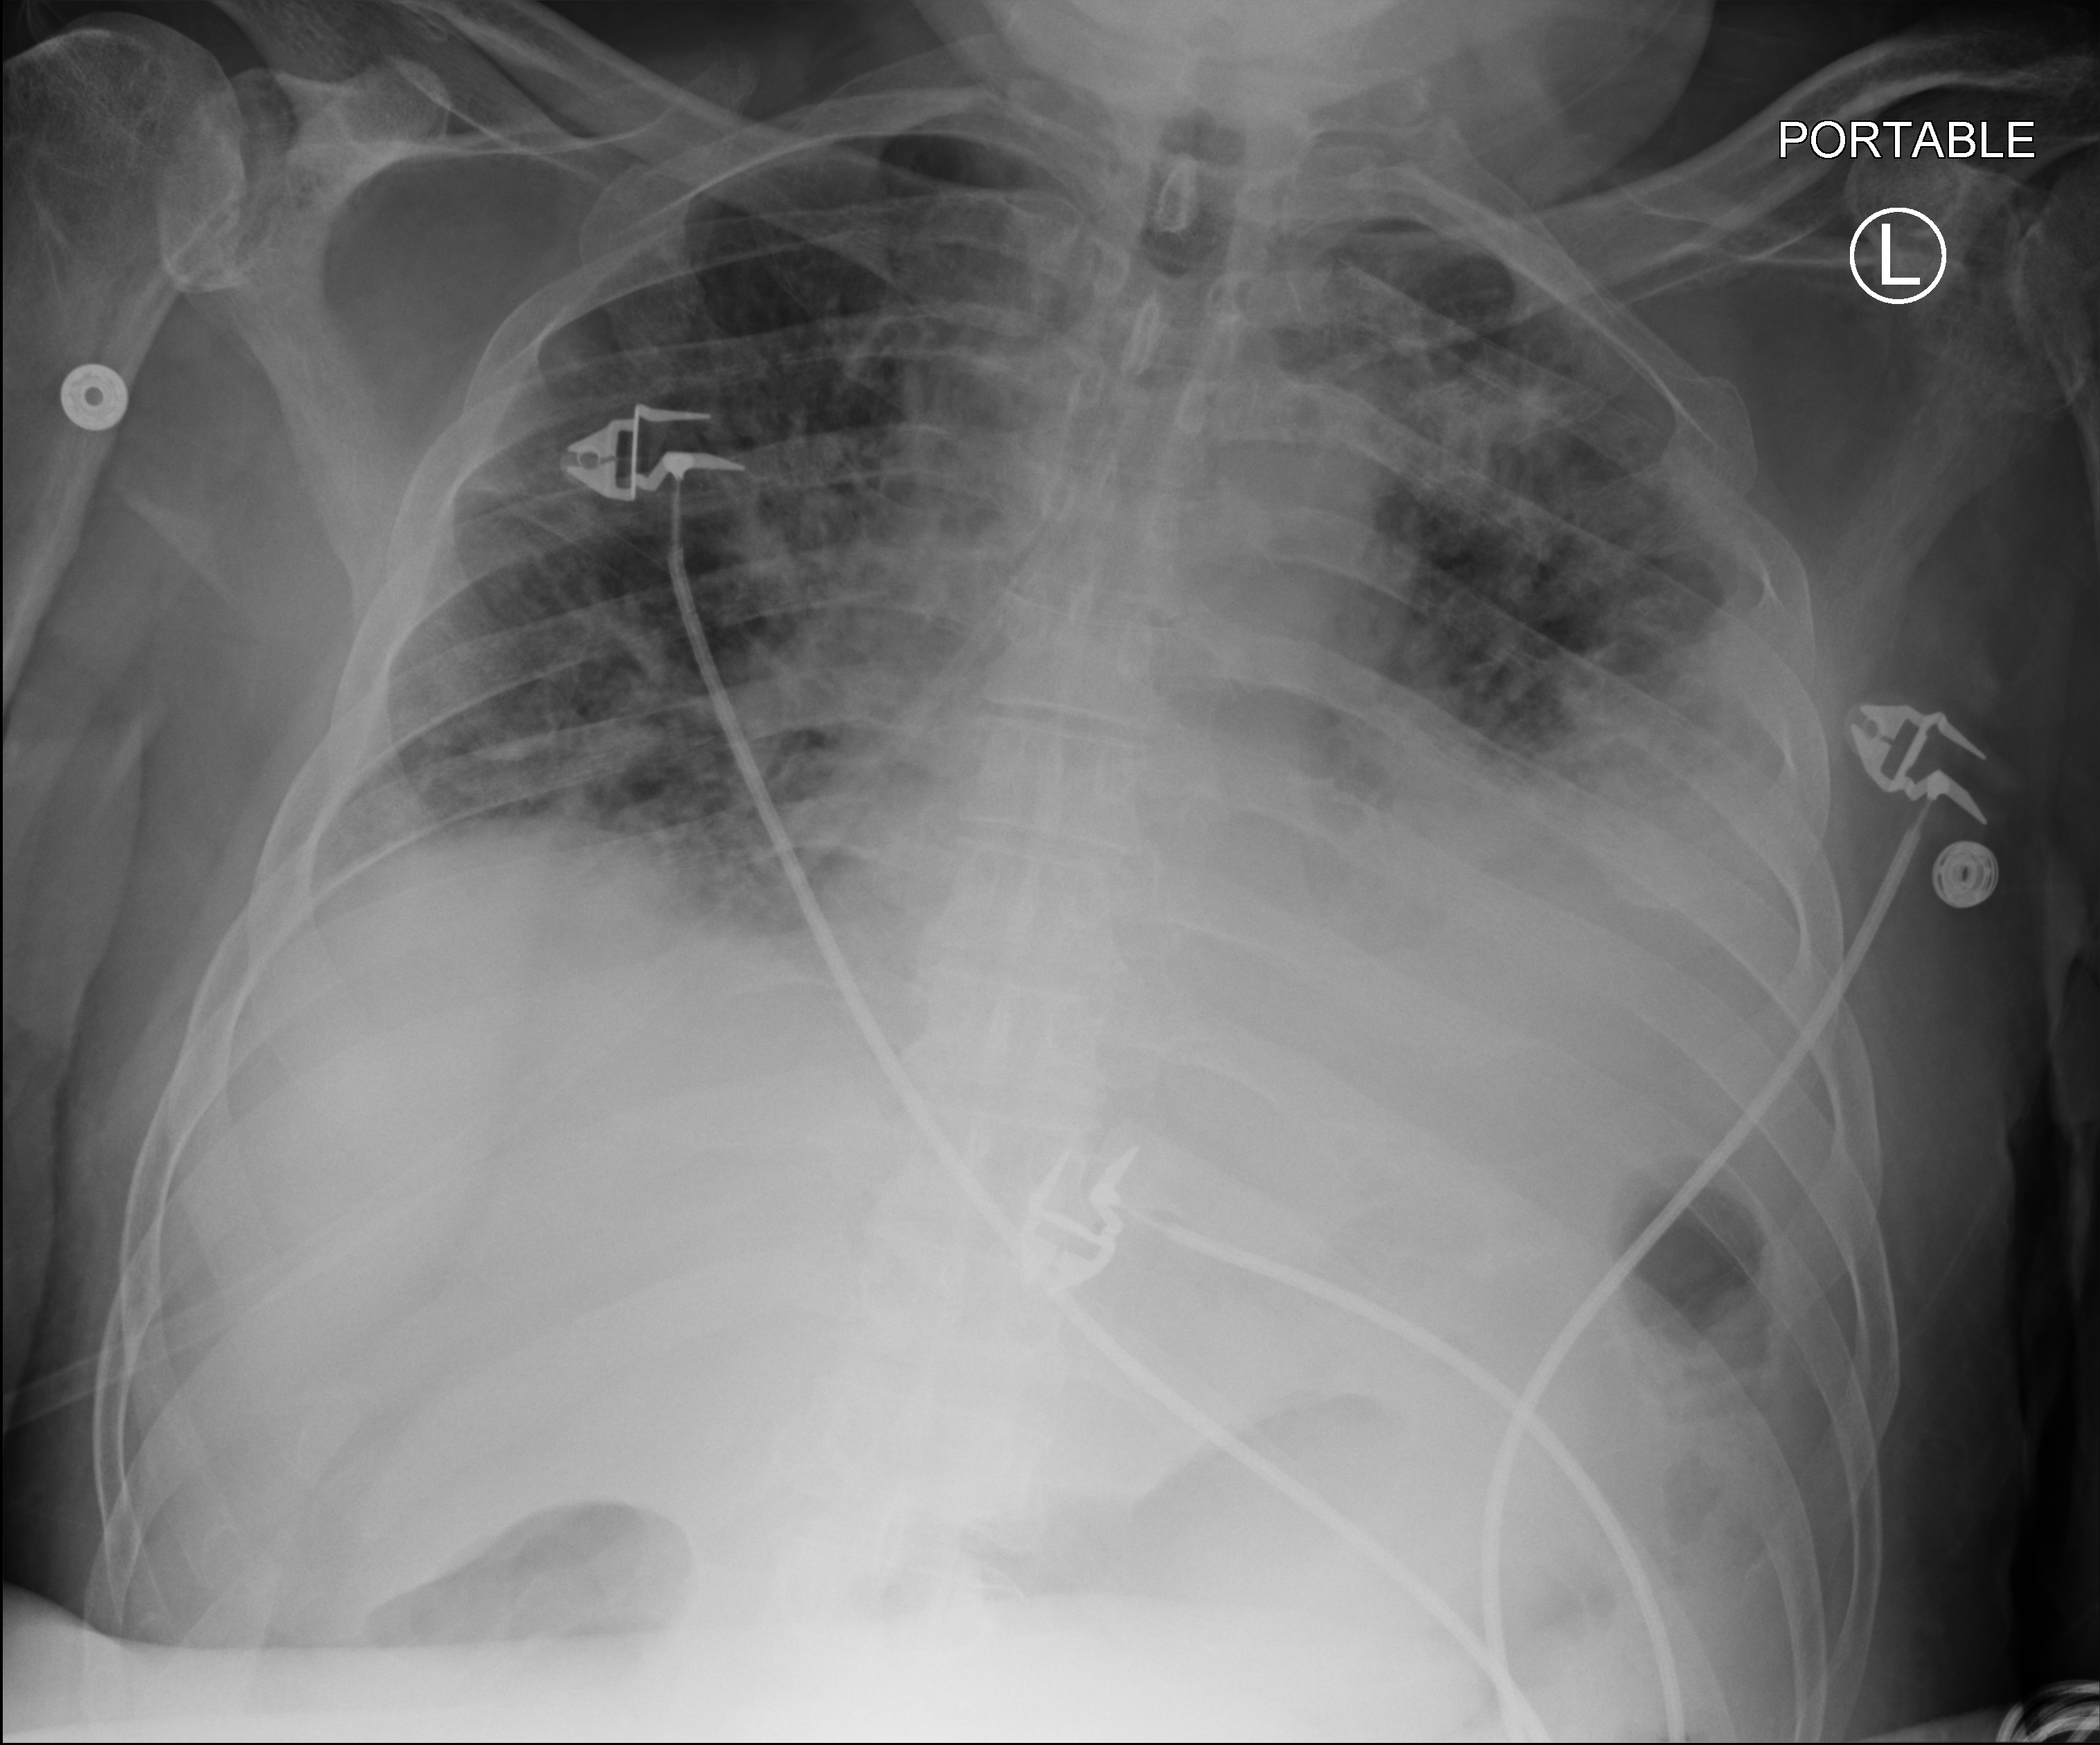
Chest X-ray (portable); anteroposterior (AP) projection. Patient hospitalised with COVID-19; male, aged 60–74 years.
Hospital-stay facts (about this admission, not read from this image; timing relative to this image not recorded):
- admitted to intensive care during this hospital stay: no